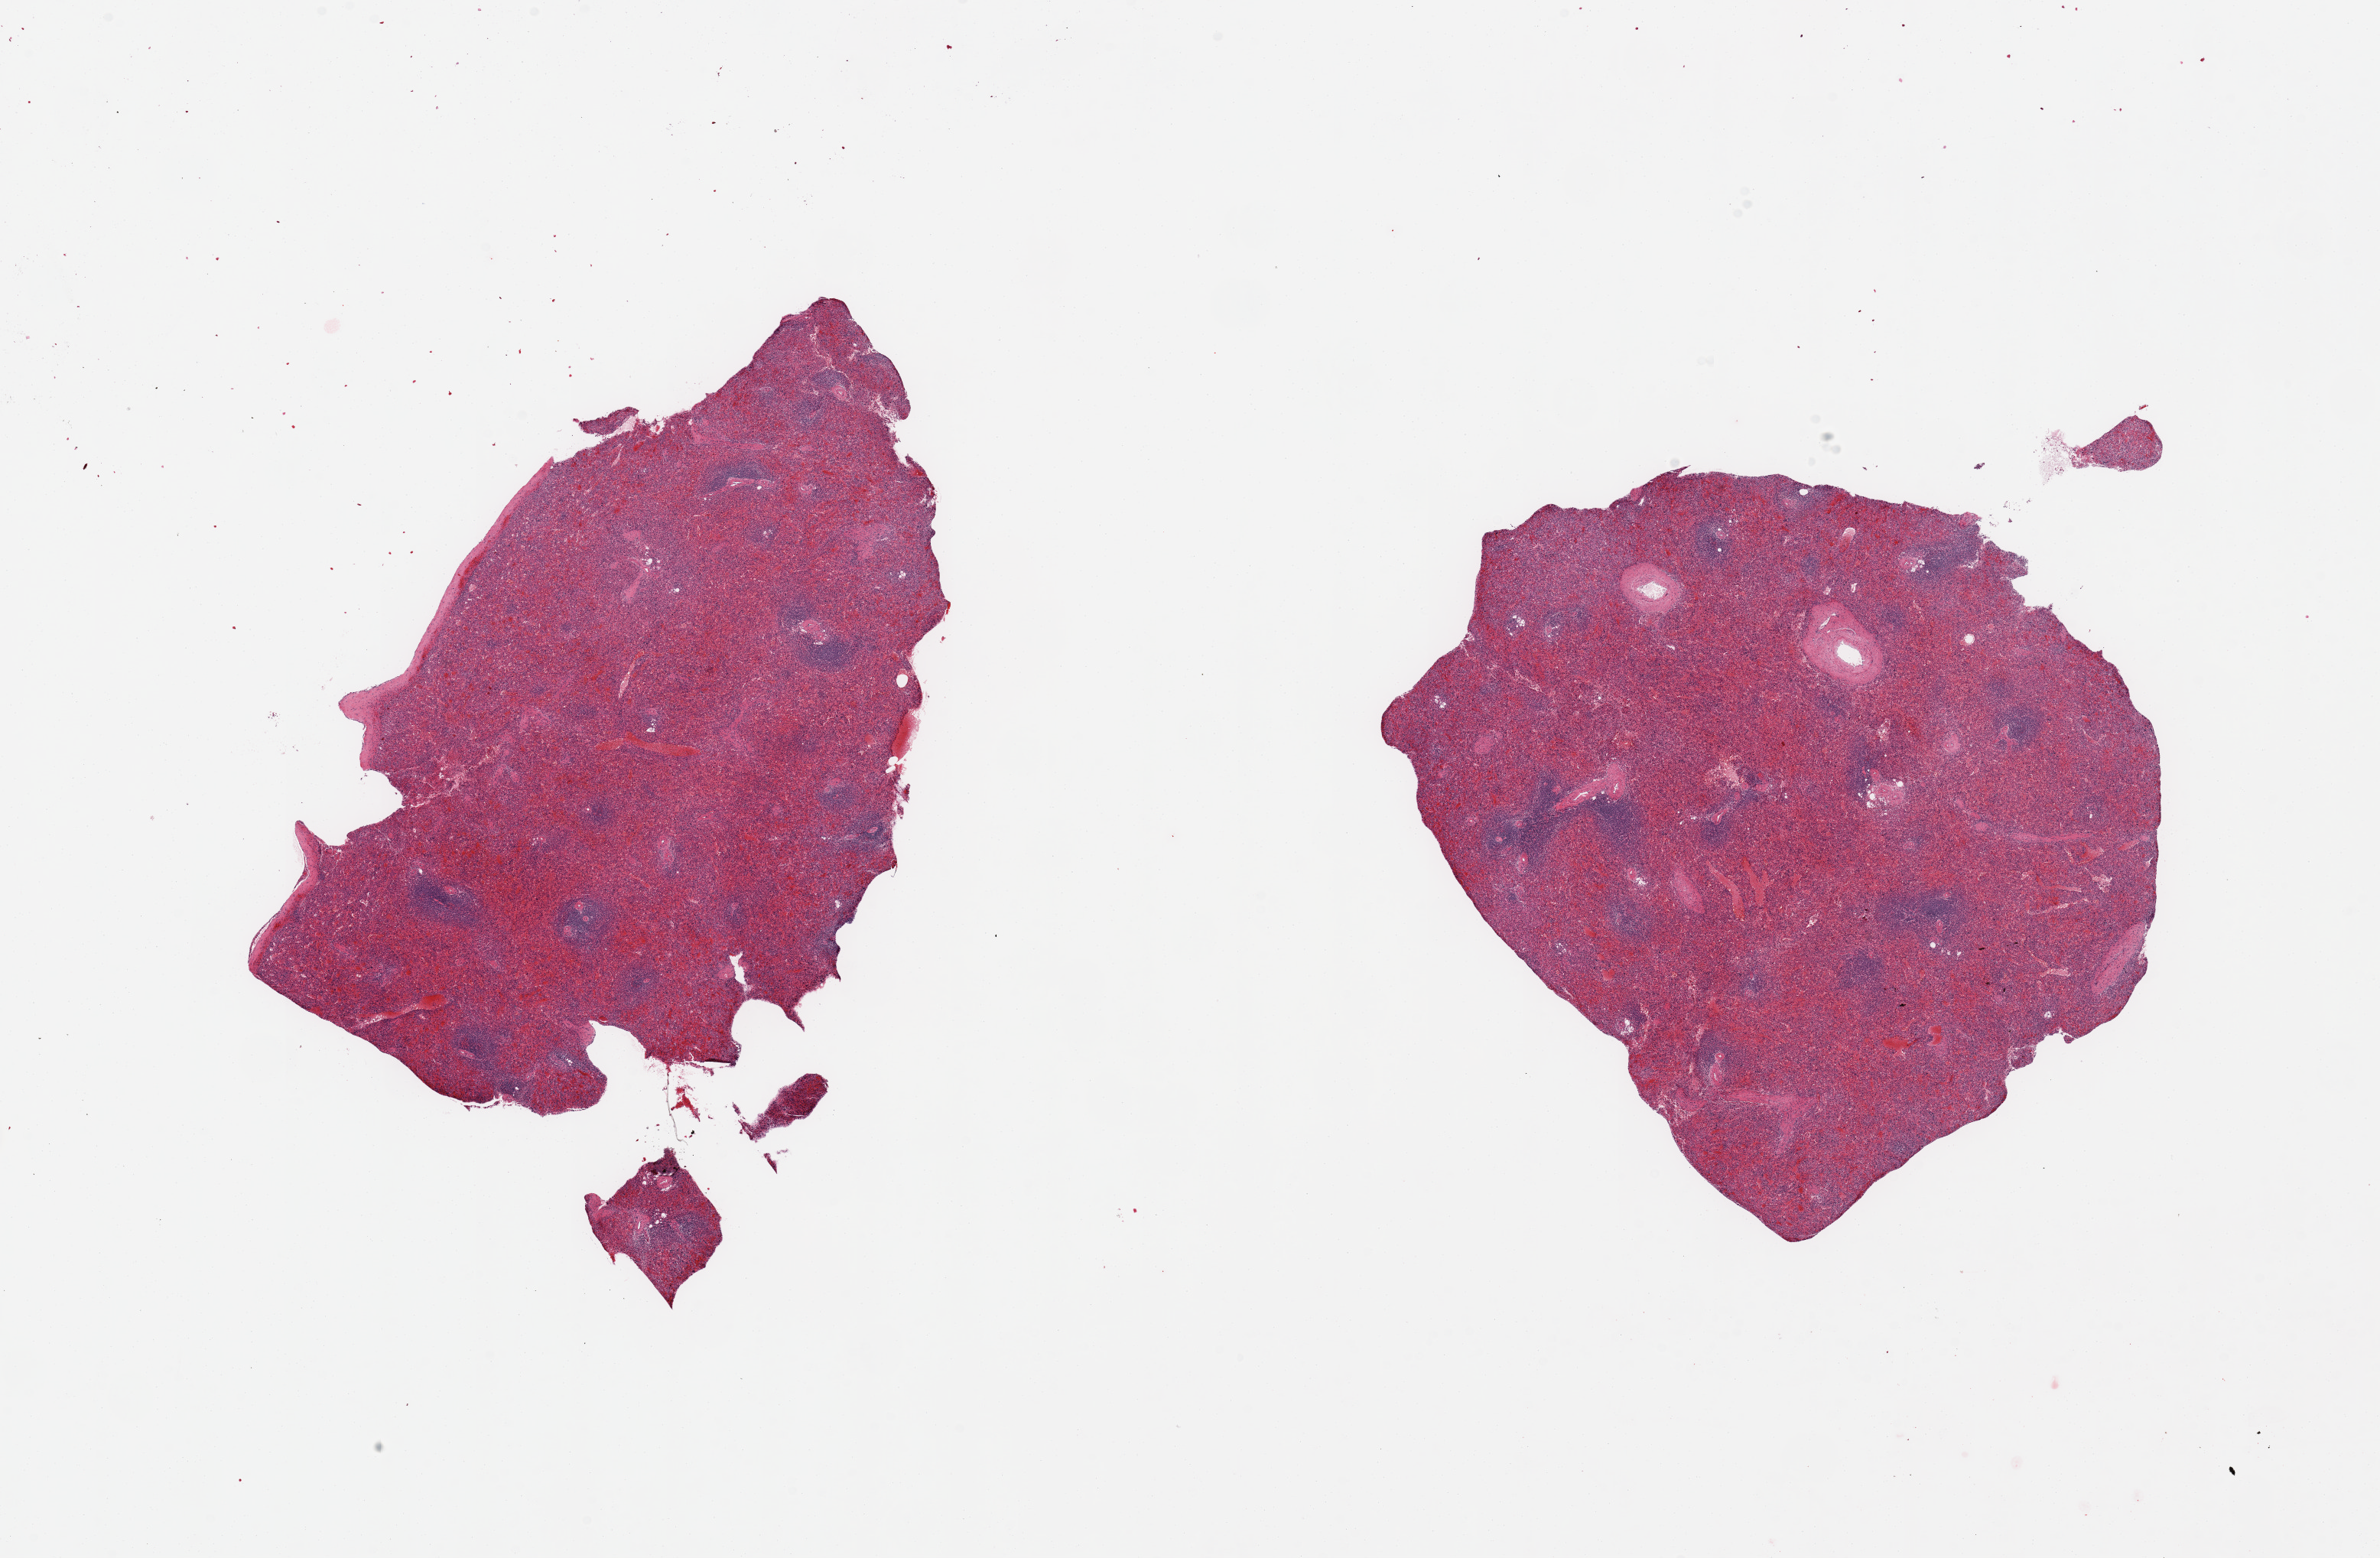
Whole-slide image, haematoxylin and eosin stain — shown as a low-resolution overview of the whole scanned area (about 24.6 x 16.1 mm, acquisition: 20x scan), PAXgene-fixed, paraffin-embedded tissue, section of spleen (target tissue), tissue donor sample. Donor sex: male.
* reviewer comment on this tissue sample: 2 pieces; capsule is present on 1 piece, some congestion